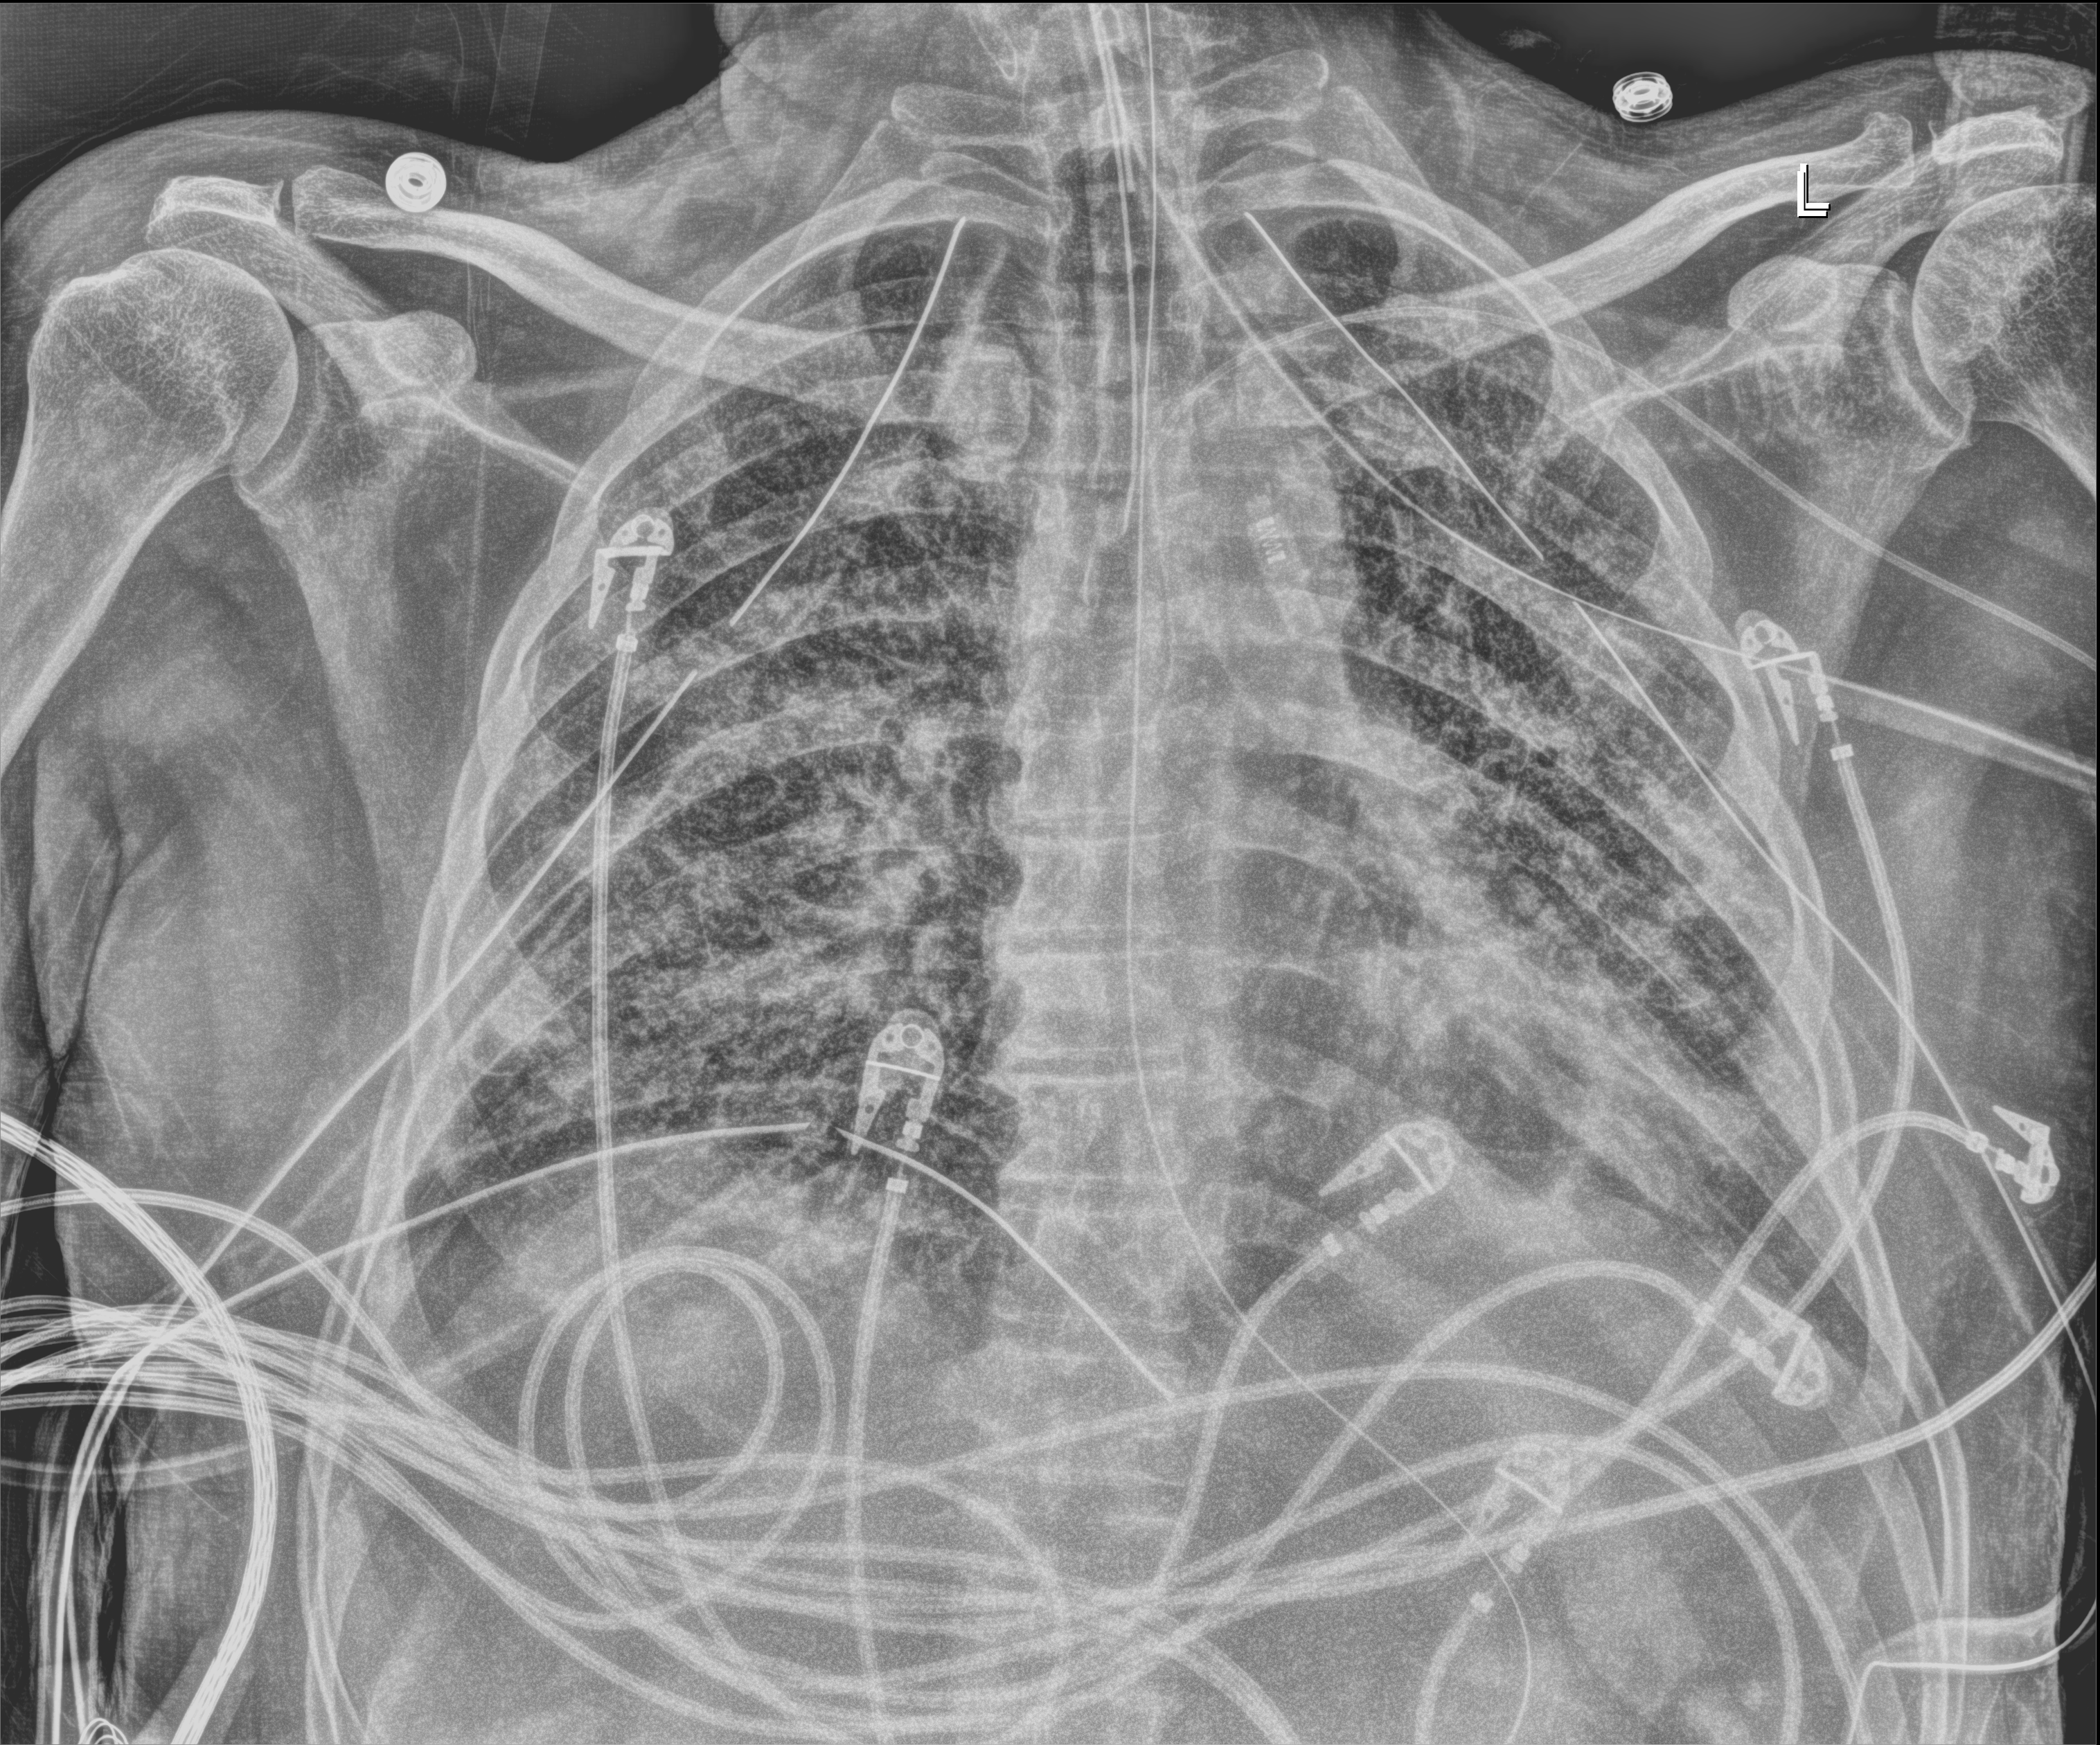
Chest X-ray (portable), anteroposterior (AP) projection. Male patient hospitalised with COVID-19, age 18–59 years.
Hospital-stay facts (about this admission, not read from this image; timing relative to this image not recorded): mechanically ventilated during this hospital stay: yes.